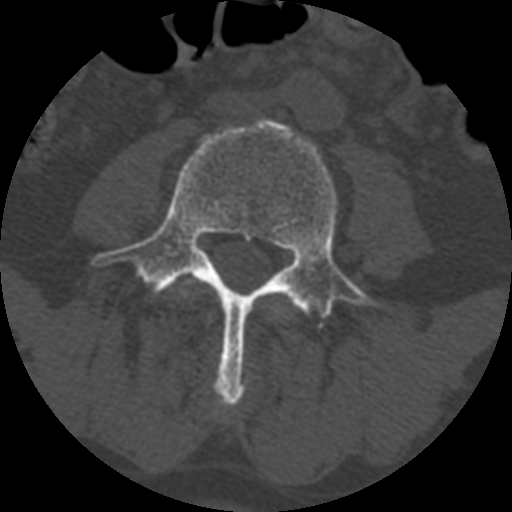
CT including the spine, one axial slice; slice 285 of 399 in the series (ordered by position); 120 kVp; bone window (W 1800 / L 400 HU); 512 × 512 image matrix. Patient age 71 years. Case-level facts recorded for this patient, not image findings: primary cancer: prostate.
Outlined on this slice (semi-automatically segmented with operator editing):
- L3 vertebra: box from (x=181, y=281) to (x=192, y=297) px
- L4 vertebra: (x=95, y=120)–(x=380, y=409)